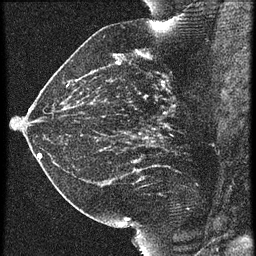
Breast MRI (dynamic contrast-enhanced), one sagittal slice; position 30 of 60 along the scan axis; 3 images stored at this slice position (order not interpretable as contrast timing); 1.5 T; TE 4.2 ms, TR 21.3 ms; 1.5 mm slice thickness; 256 × 256 image matrix, field of view 180 × 180 mm. Patient: female, 42 years. Case-level facts recorded for this patient, not image findings: setting: breast cancer imaged before/during neoadjuvant chemotherapy; receptor status: HER2-positive.
Outlined on this slice (semi-automatic segmentation, software-assisted and operator-edited):
- analysis volume of interest (the breast-tissue region the enhancement analysis was run in; not a lesion): bounding box (x1, y1, x2, y2) in pixels: (122, 82, 195, 147)
- tumour enhancement mask (voxels above the 90 % enhancement threshold inside the analysis volume of interest): (144, 82, 167, 127)